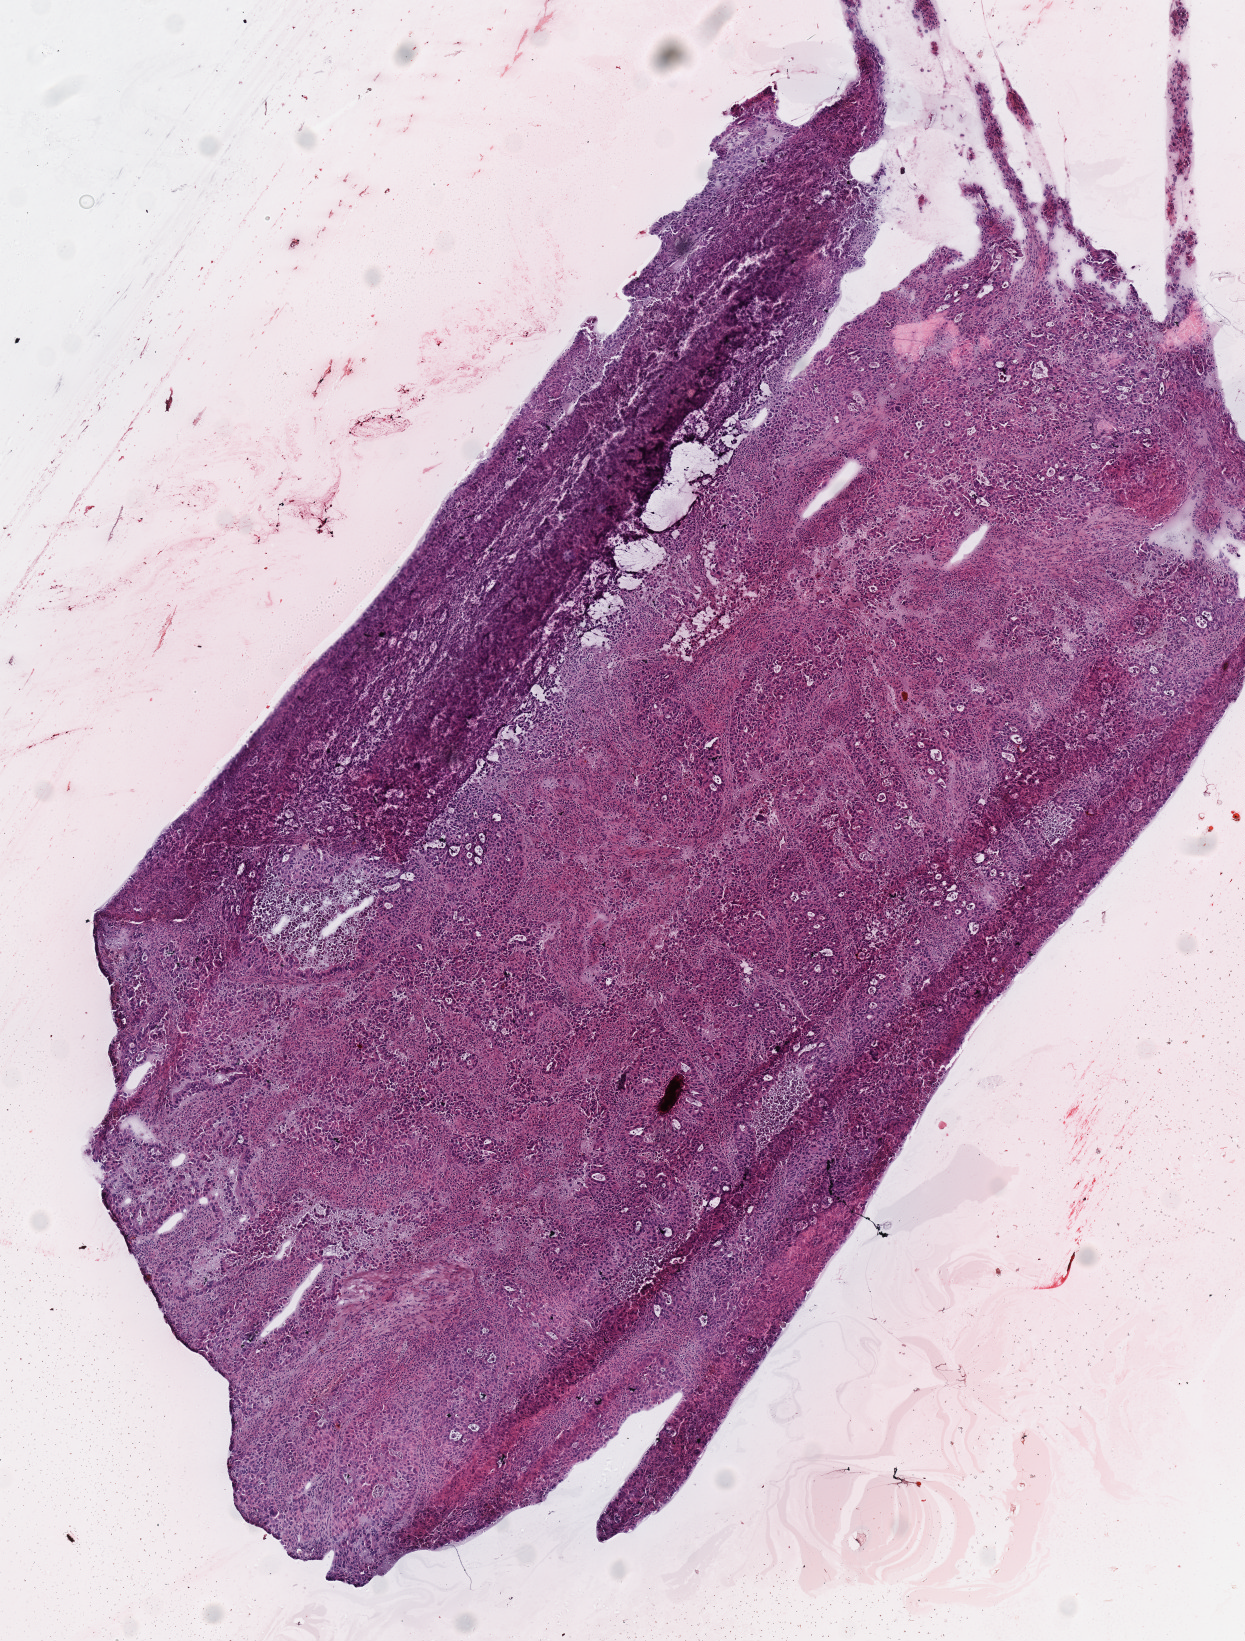
Digitized H&E-stained tissue section (whole slide), shown as a low-resolution overview of the whole scanned area (about 4.9 x 6.5 mm, slide scanned at 40x). Frozen section from the top of the tissue portion. Sample: primary tumour, lung. Patient: female, age at initial diagnosis 73 years. Slide review estimates, as recorded: tumour cells 83%, tumour nuclei 70%, normal cells 0%, stromal cells 10%, necrosis 7%. Infiltration values recorded for this section: lymphocyte infiltration 25%.
* AJCC pathologic stage: IIIA (6th edition)
* laterality: right
* histologic diagnosis: Adenocarcinoma with mixed subtypes (upper lobe, lung)